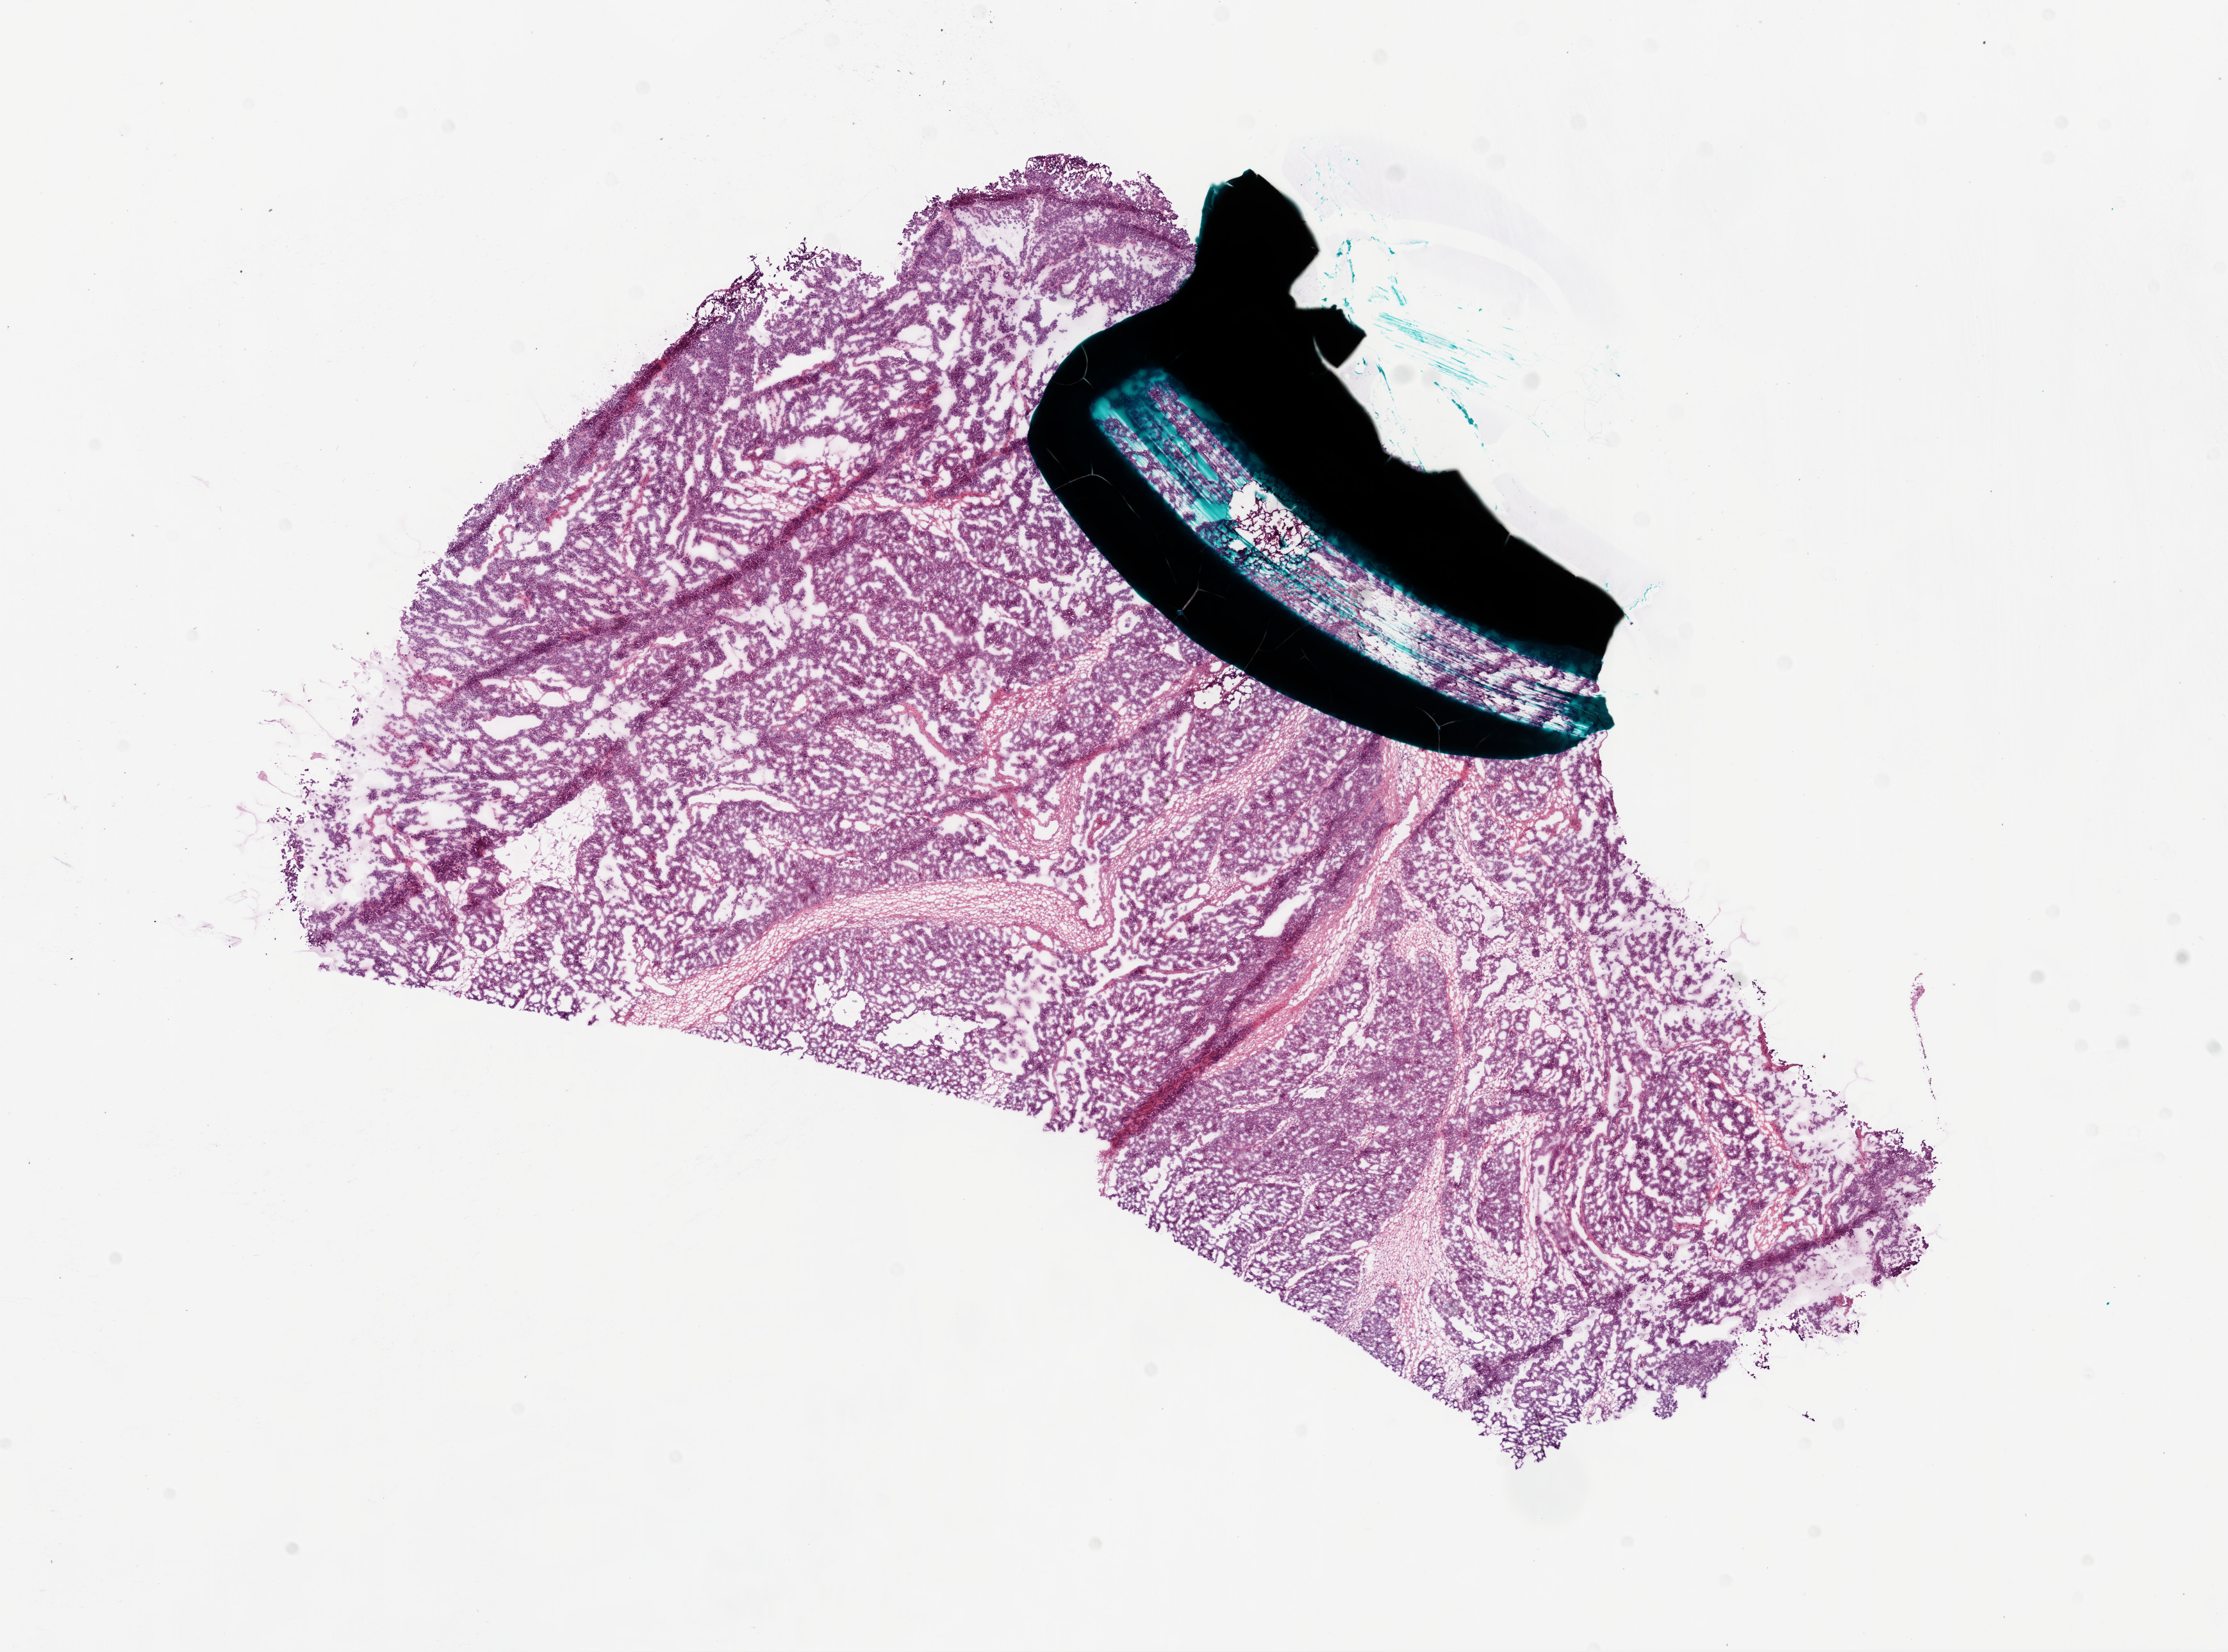
Digitized H&E tissue section (whole slide) — low-resolution overview of the scanned area, about 14.0 x 10.4 mm (slide scanned at 20x), frozen section from the bottom of the tissue portion, ovary, primary tumour sample. Female, age 69 years at initial diagnosis. Histologic grade: G3 (poorly differentiated). Slide review estimates, as recorded: tumour cells 90%, tumour nuclei 90%, normal cells 5%, stromal cells 5%, necrosis 0%.
FIGO stage: IIIC. Diagnosis: Serous cystadenocarcinoma, NOS.